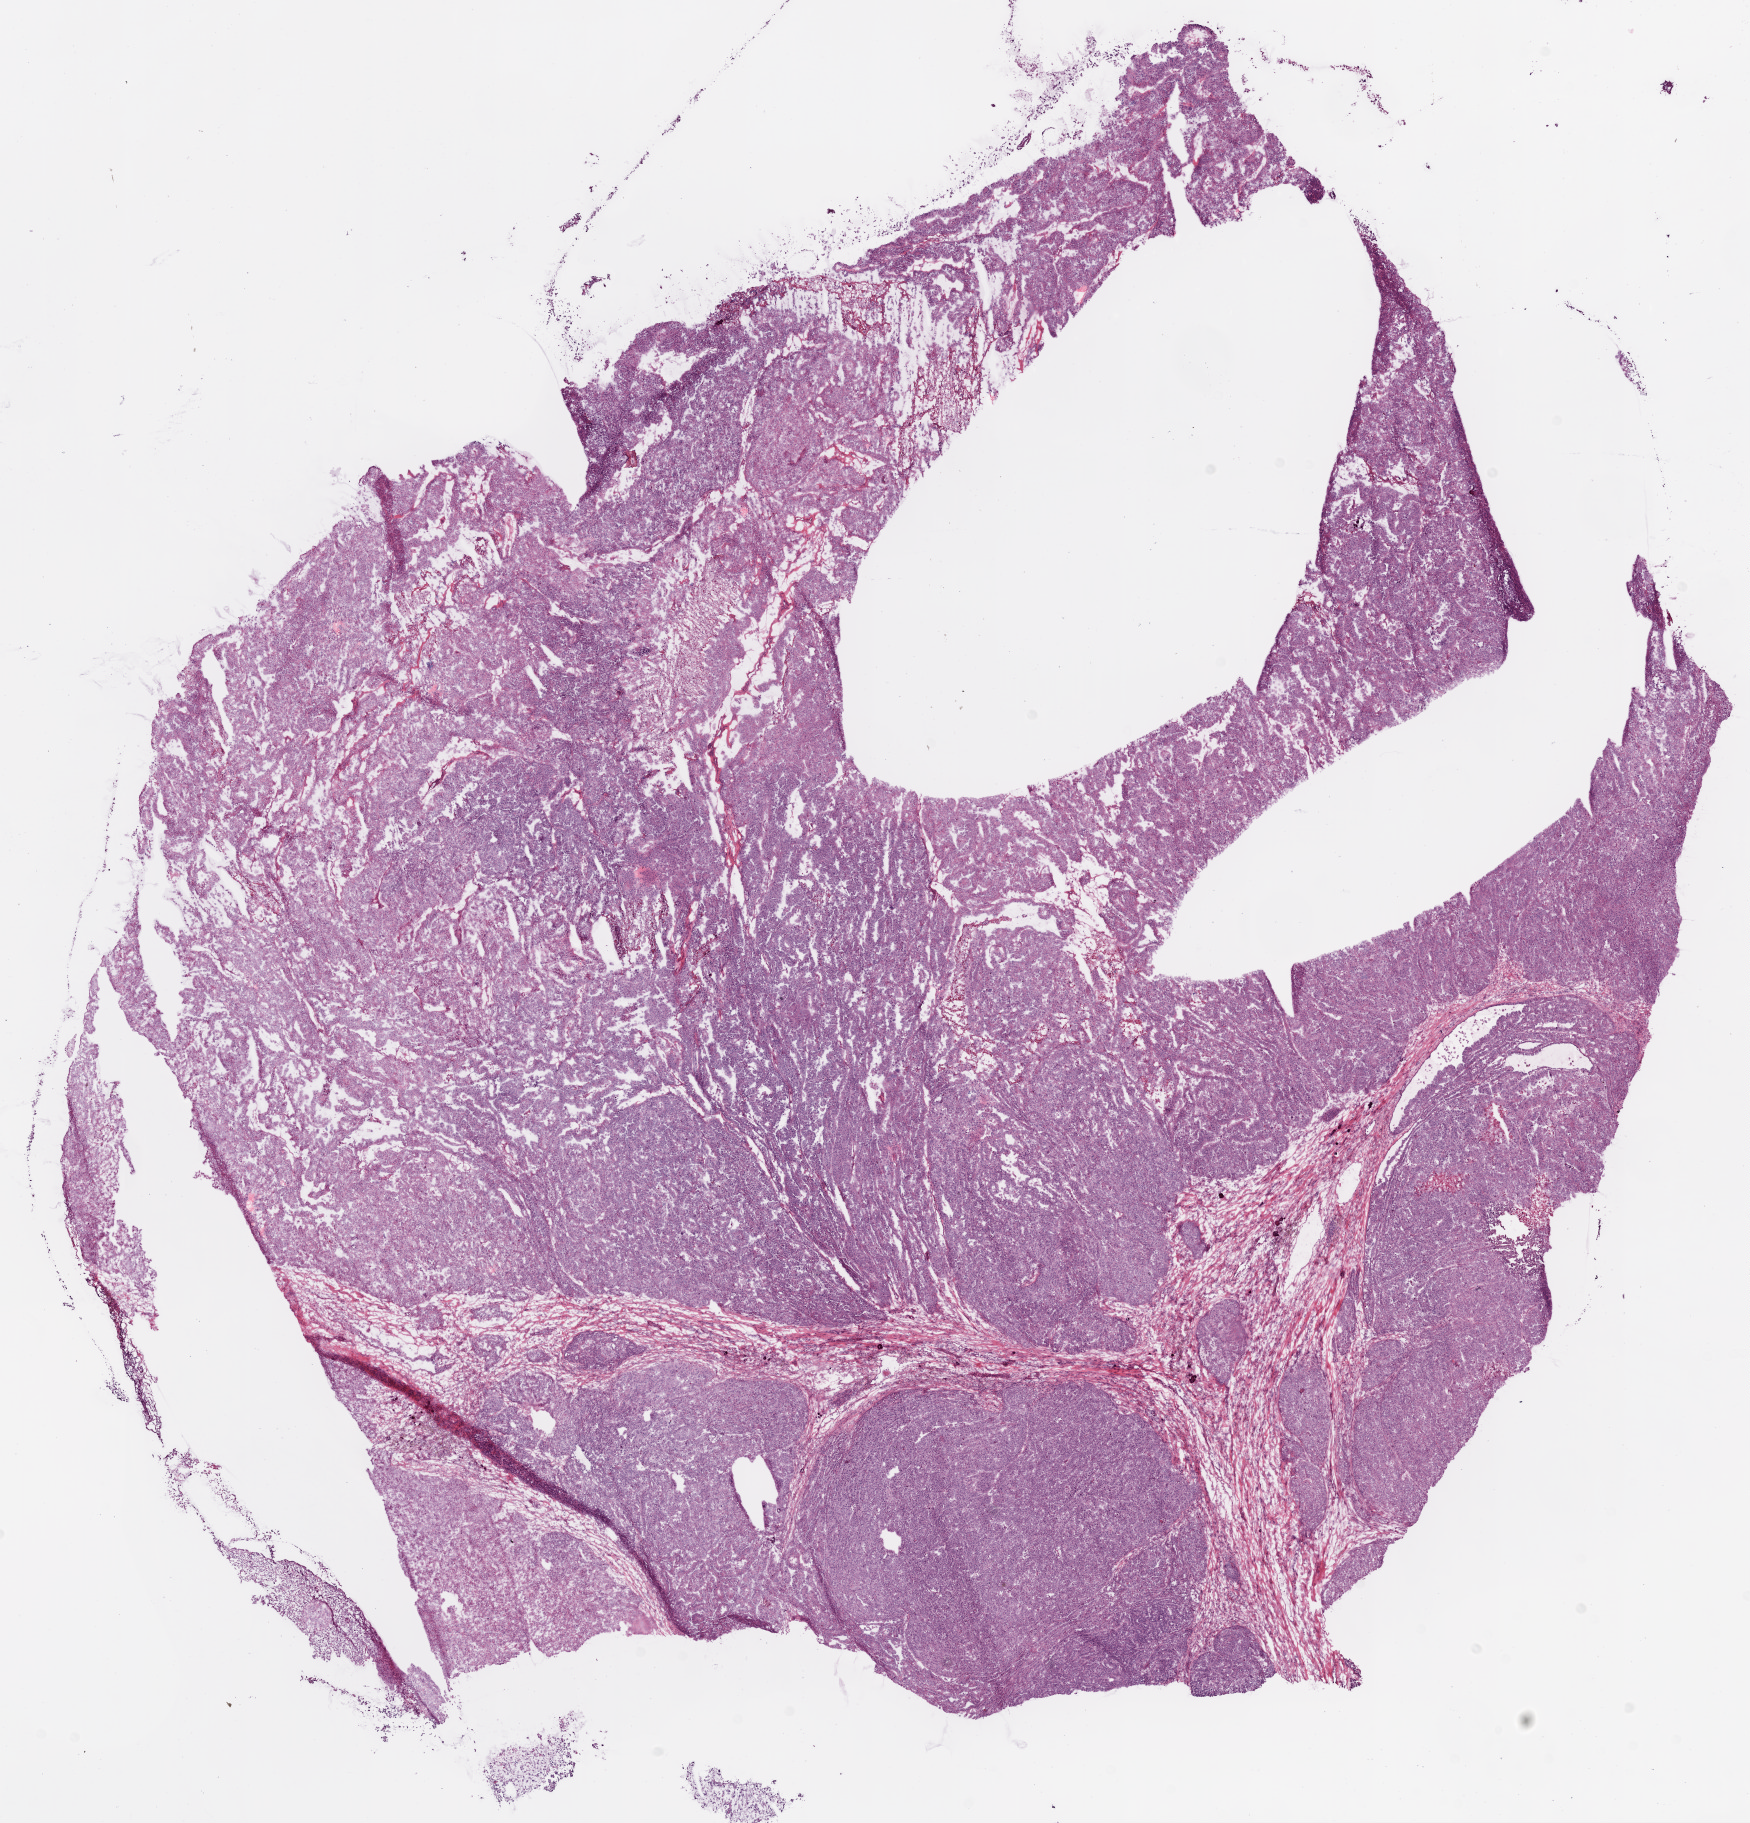
Whole-slide histology image, Hematoxylin and eosin (H&E) stained — shown as a low-resolution overview of the whole scanned area (about 14.0 x 14.6 mm, slide scanned at 20x); frozen section from the bottom of the tissue portion; primary tumour sample from the ovary. Patient: female, age at initial diagnosis 60 years. Histologic grade: G3 (poorly differentiated). Pathologist review of this section (percent, as recorded): tumour cells 95%, tumour nuclei 90%, normal cells 0%, stromal cells 0%, necrosis 5%. Infiltration values recorded for this section: lymphocyte infiltration 3%, monocyte infiltration 2%.
* laterality: right
* FIGO stage: IIIC
* histologic diagnosis: Serous cystadenocarcinoma, NOS